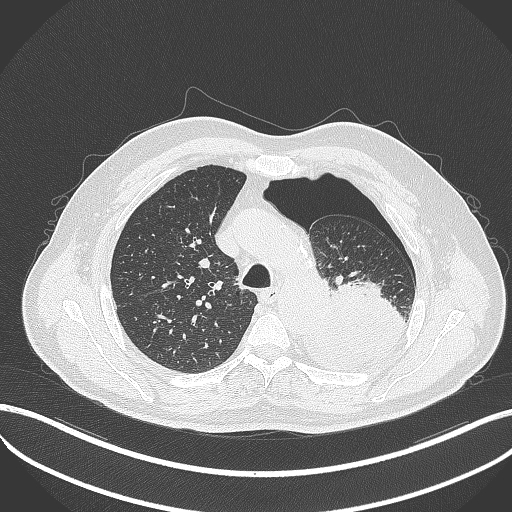
Chest CT, one axial slice; position 374 of 464 along the scan axis; lung window (W 1500 / L -600 HU); 1 mm slice thickness; 512 × 512 image matrix. Male patient, age 76 years. From the clinical record (not read from this slice): clinical TNM (as recorded): T3 N0 M1b.
Structures marked on this image (rectangle marked by the reading radiologist):
- lung tumour (recorded histology: adenocarcinoma): box from (x=294, y=271) to (x=410, y=376) px